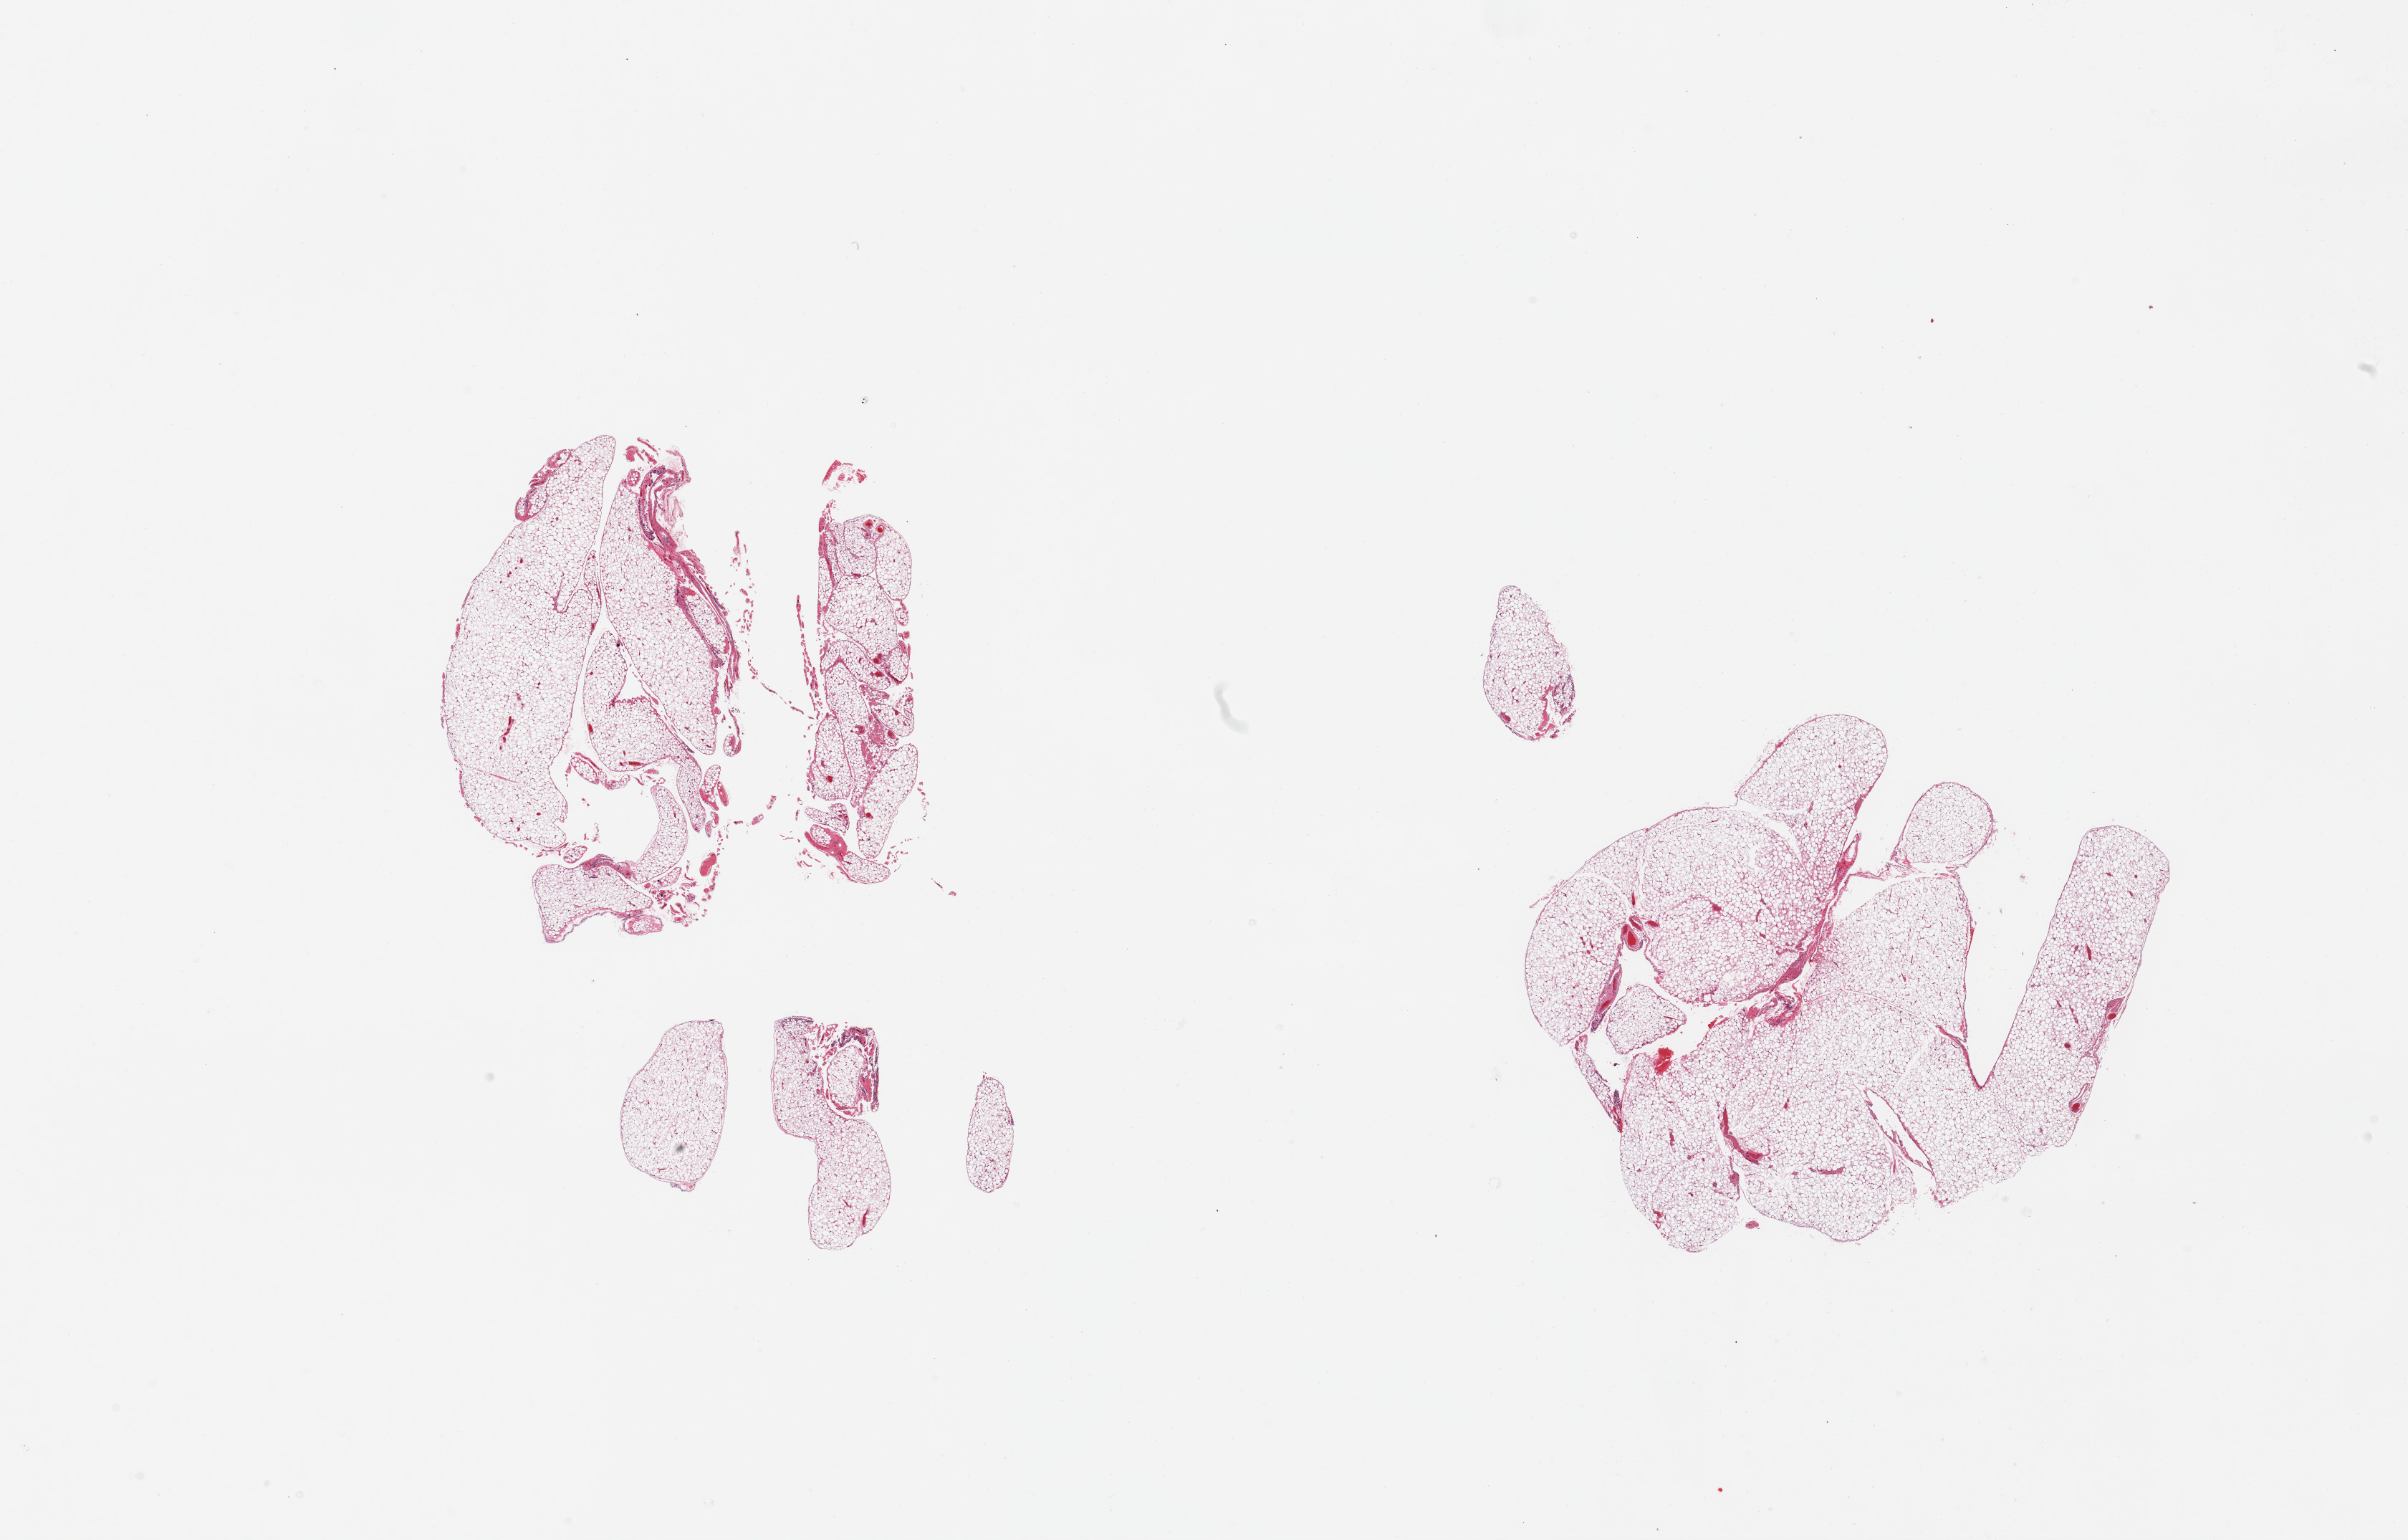
Digitized hematoxylin and eosin (H&E)-stained section — shown as a low-resolution overview of the whole scanned area (about 26.6 x 17.0 mm, from a 20x scan). PAXgene-fixed, paraffin-embedded tissue. Sampled site (target tissue): omentum. Tissue donor sample. Donor: male.
Reviewer comment on this tissue sample: 2 fragmented pieces.